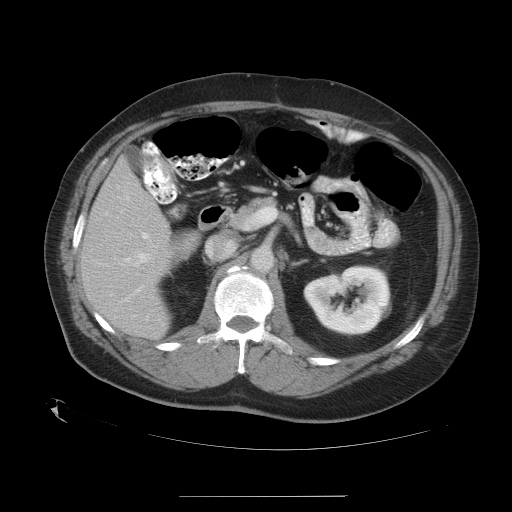
Contrast-enhanced abdominal CT, one axial slice; position 16 of 35 along the scan axis; reconstruction kernel STANDARD; 120 kVp; intravenous contrast given; soft-tissue window (W 400 / L 40 HU); 7.5 mm slice thickness; 512 × 512 image matrix, field of view 450 × 450 mm. Male patient, age 67 years. From the clinical record (not read from this slice): diagnosis: colorectal cancer liver metastases, imaged before liver resection; multiple liver metastases: no; largest metastasis: 2.3 cm; disease in both lobes: no.
Structures marked on this image (outlined manually by an expert reader):
- hepatic veins: box from (x=126, y=197) to (x=129, y=200) px
- liver: (x=83, y=161)–(x=172, y=338)
- planned liver remnant (the part of the liver to remain after resection): (x=83, y=160)–(x=171, y=338)
- portal vein (with intrahepatic branches): (x=132, y=233)–(x=149, y=291)